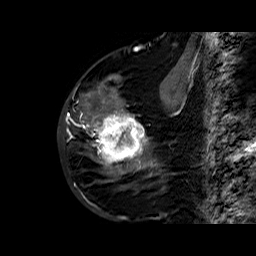
Breast MRI (dynamic contrast-enhanced), one sagittal slice. Position 21 of 60 along the scan axis. Dynamic contrast-enhanced series, time point 2 of 6 at this slice position (early post-contrast). 1.5 T. TE 6.4 ms, TR 32.8 ms. 256 × 256 image matrix, field of view 200 × 200 mm. Female patient. From the clinical record (not read from this slice): setting: breast cancer imaged before/during neoadjuvant chemotherapy; receptor status: HR-positive, HER2-negative.
Outlined on this slice (semi-automatically segmented with operator editing):
- analysis volume of interest (the breast-tissue region the enhancement analysis was run in; not a lesion): bounding box (x1, y1, x2, y2) in pixels: (86, 77, 163, 177)
- tumour enhancement mask (voxels above the 100 % enhancement threshold inside the analysis volume of interest): (91, 90, 152, 170)